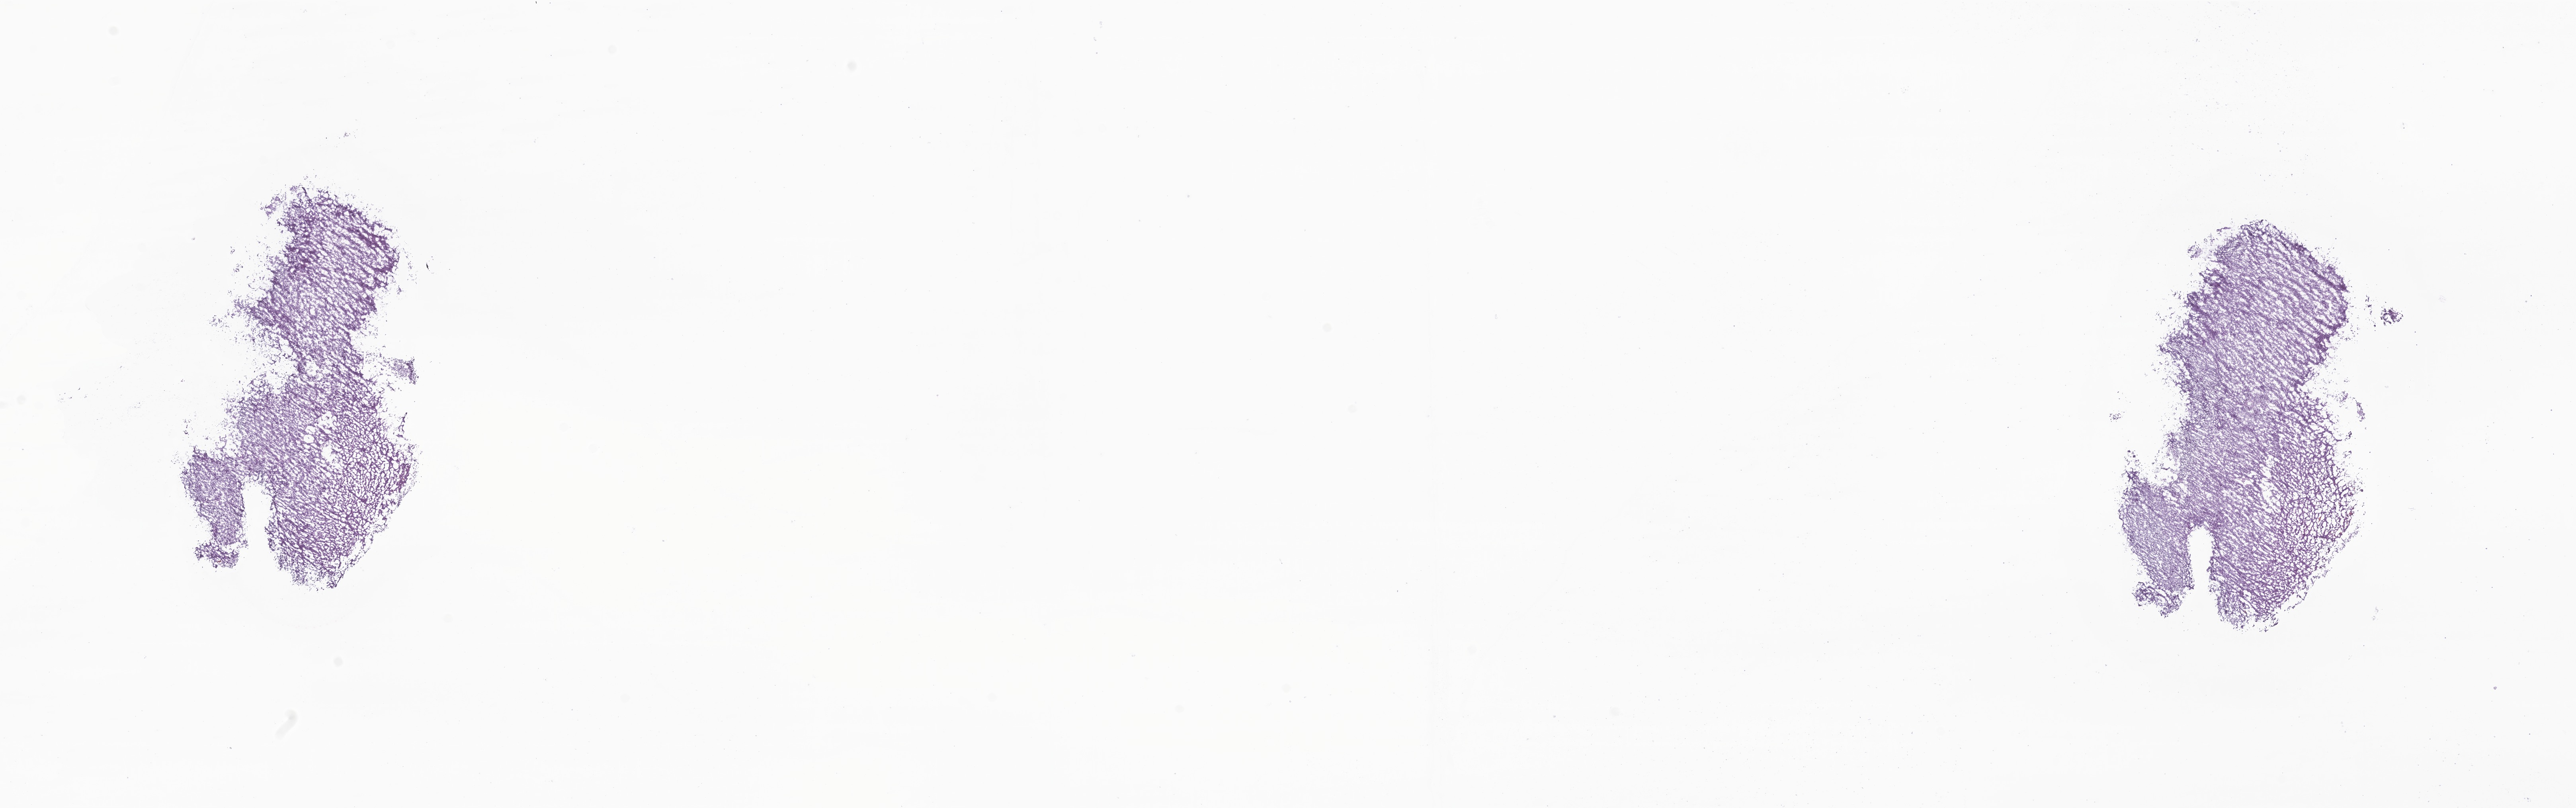
Whole-slide image, haematoxylin and eosin stain of tumor tissue from the brain — a low-resolution overview of the entire scanned area, about 27.3 x 8.6 mm. Cryosection (OCT / tissue freezing medium). Patient male; age 666 days (about 1.8 years).
- diagnosis: Medulloblastoma, NOS